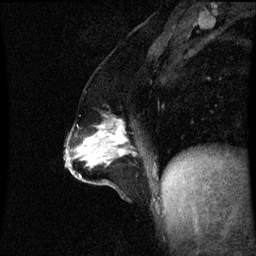
Breast MRI (dynamic contrast-enhanced), one sagittal slice. Slice 29 of 60 in the series (ordered by position). Dynamic contrast-enhanced series, image 2 of 3 at this slice position (ordered by acquisition). 1.5 T. TE 4.2 ms, TR 8.9 ms. 2.1 mm slice thickness. 256 × 256 image matrix, field of view 200 × 200 mm. Patient: female, 47 years. Case-level facts recorded for this patient, not image findings: setting: breast cancer imaged before/during neoadjuvant chemotherapy; receptor status: HR-positive, HER2-negative.
Annotated regions visible in this slice (semi-automatically segmented with operator editing):
- analysis volume of interest (the breast-tissue region the enhancement analysis was run in; not a lesion): bounding box <71,122,137,163> (left, top, right, bottom; pixels)
- tumour enhancement mask (voxels above the 70 % enhancement threshold inside the analysis volume of interest): <87,126,126,155>